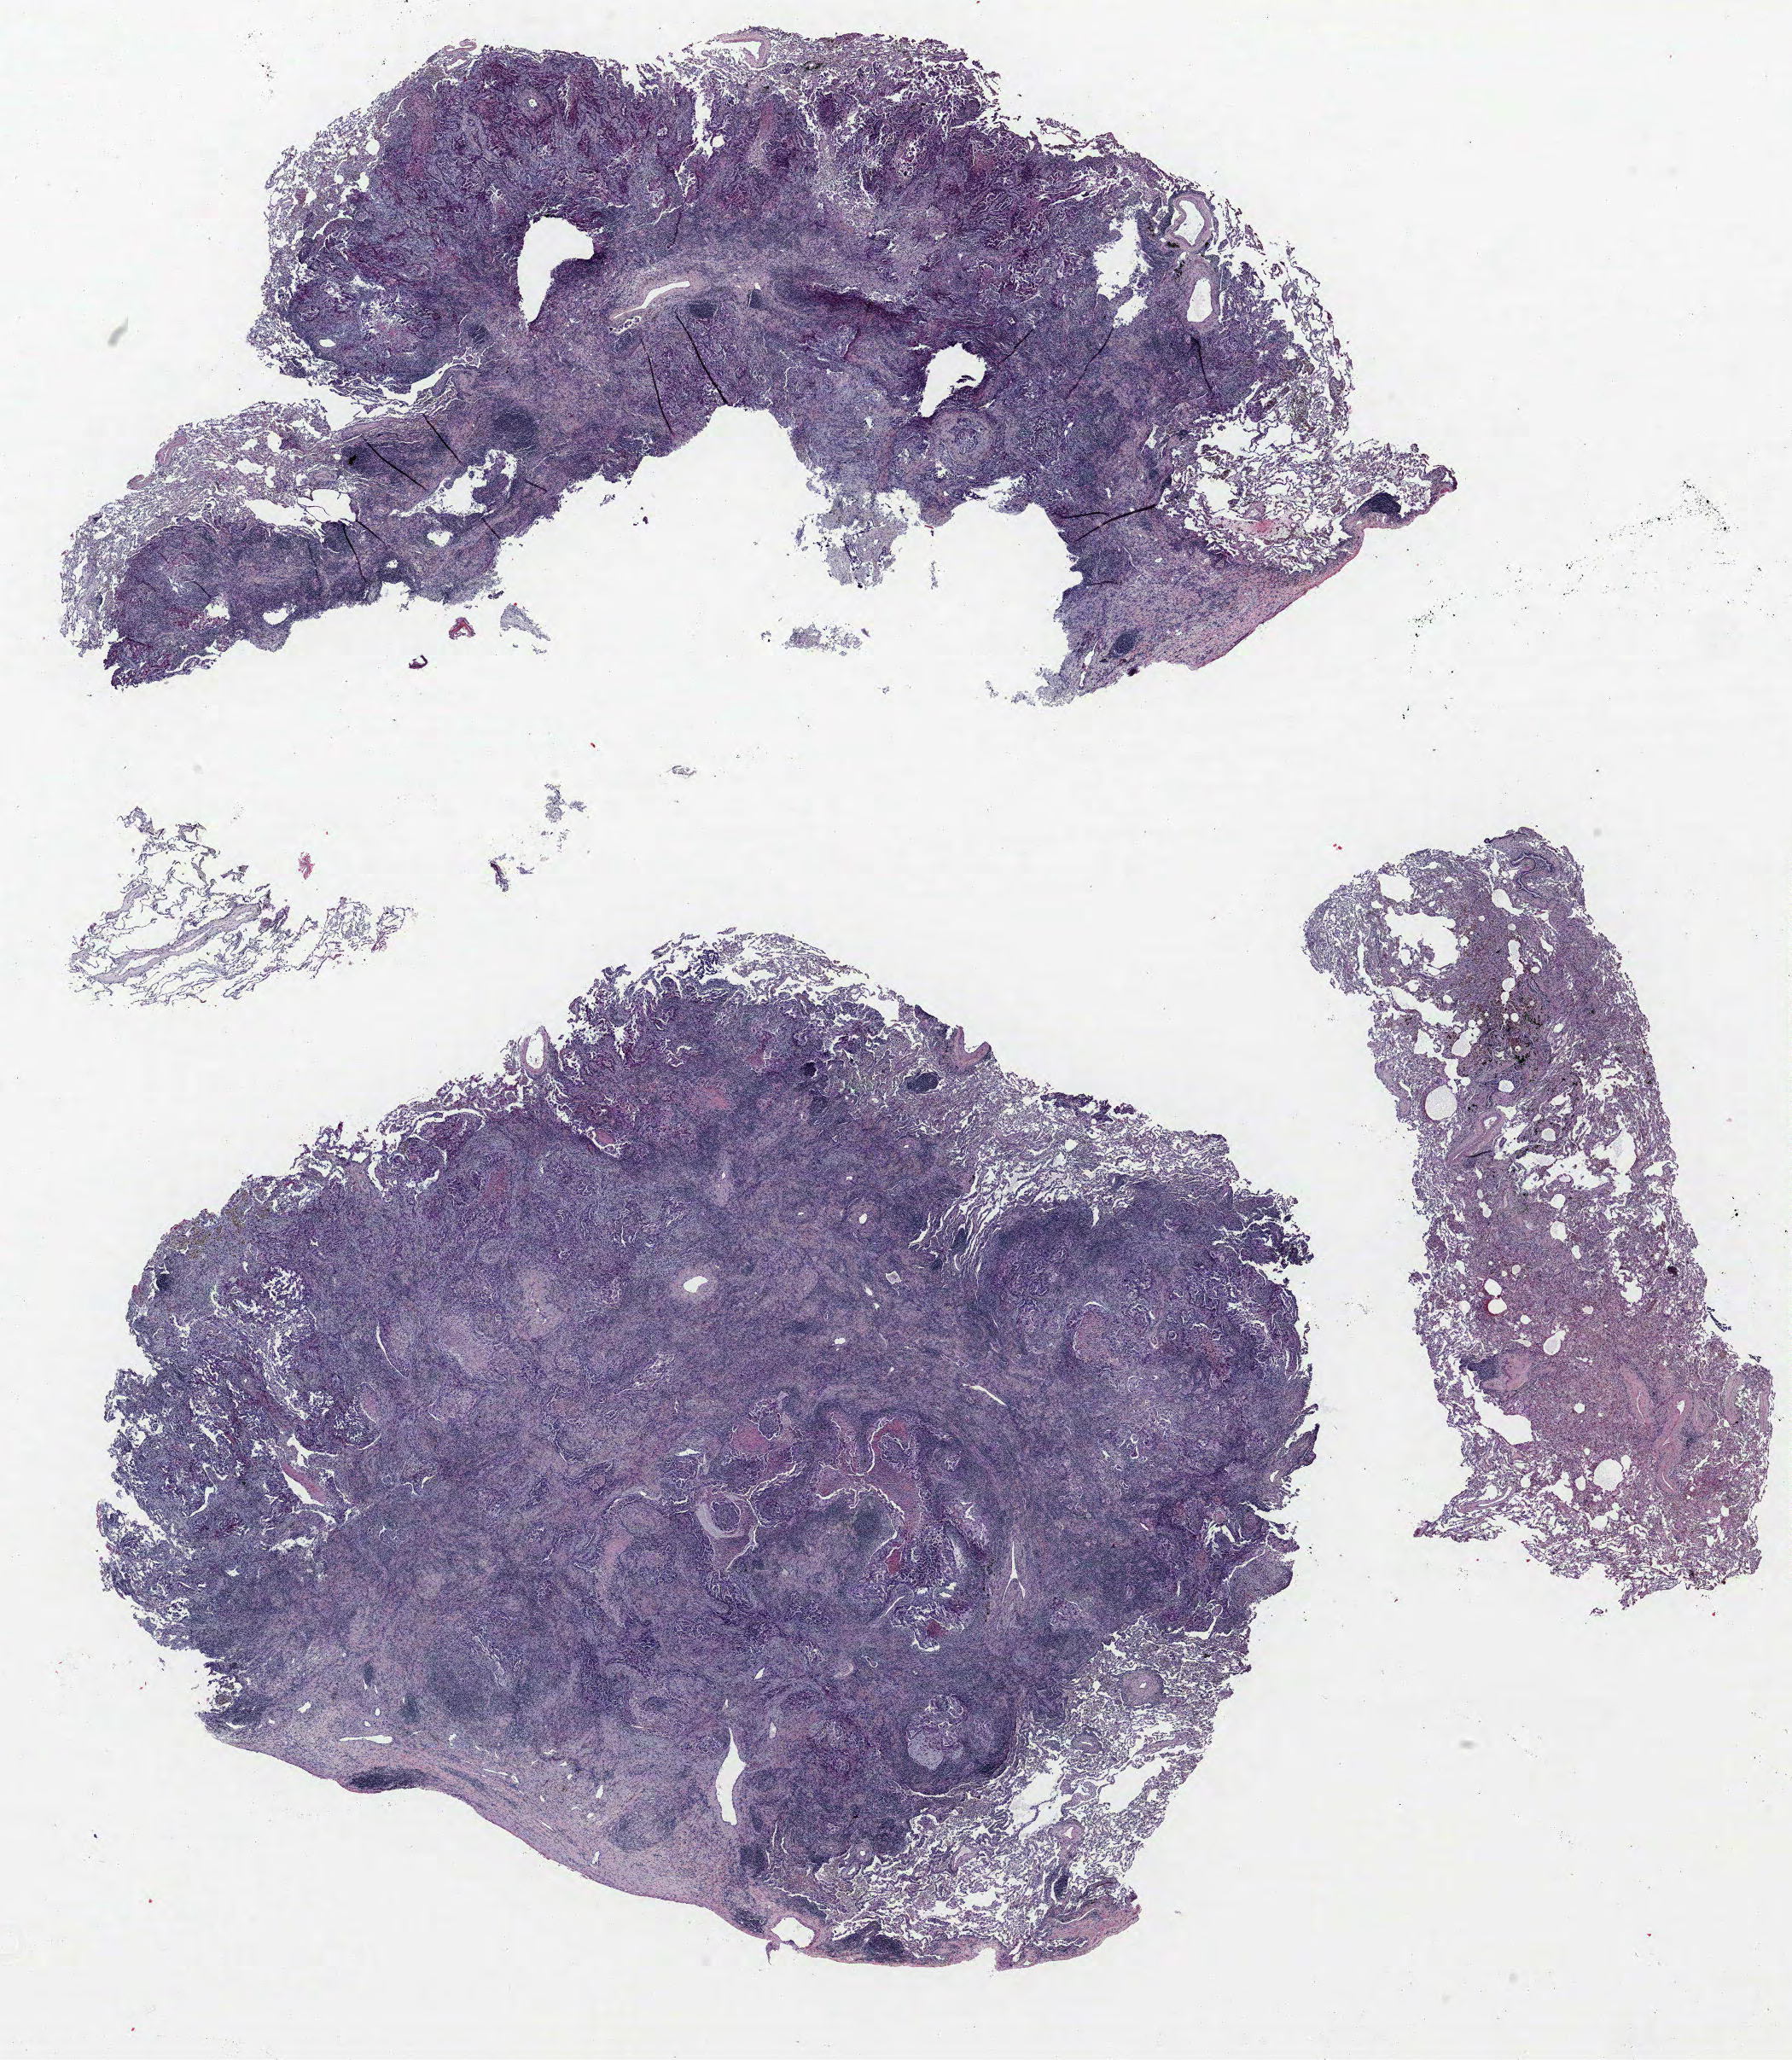
Whole-slide histology image, Hematoxylin and eosin (H&E) stained, shown as a low-resolution overview of the whole scanned area (about 16.8 x 19.3 mm); FFPE section; lung tissue. Male, age 73 at enrolment.
Participant's lung-cancer diagnosis: Adenocarcinoma, NOS.